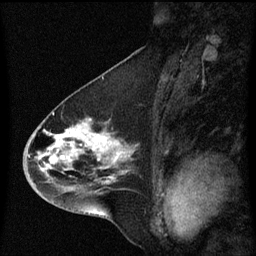
Breast MRI (dynamic contrast-enhanced), one sagittal slice; slice 31 of 60 in the series (ordered by position); dynamic contrast-enhanced series, image 2 of 3 at this slice position (ordered by acquisition); 1.5 T; TE 4.2 ms, TR 8.4 ms; 2 mm slice thickness; 256 × 256 image matrix, field of view 200 × 200 mm. Patient: female, 46 years. From the clinical record (not read from this slice): setting: breast cancer imaged before/during neoadjuvant chemotherapy; receptor status: HER2-positive.
Structures marked on this image (semi-automatically segmented with operator editing):
- analysis volume of interest (the breast-tissue region the enhancement analysis was run in; not a lesion): box from (x=23, y=112) to (x=139, y=195) px
- tumour enhancement mask (voxels above the 70 % enhancement threshold inside the analysis volume of interest): (x=42, y=134)–(x=122, y=183)